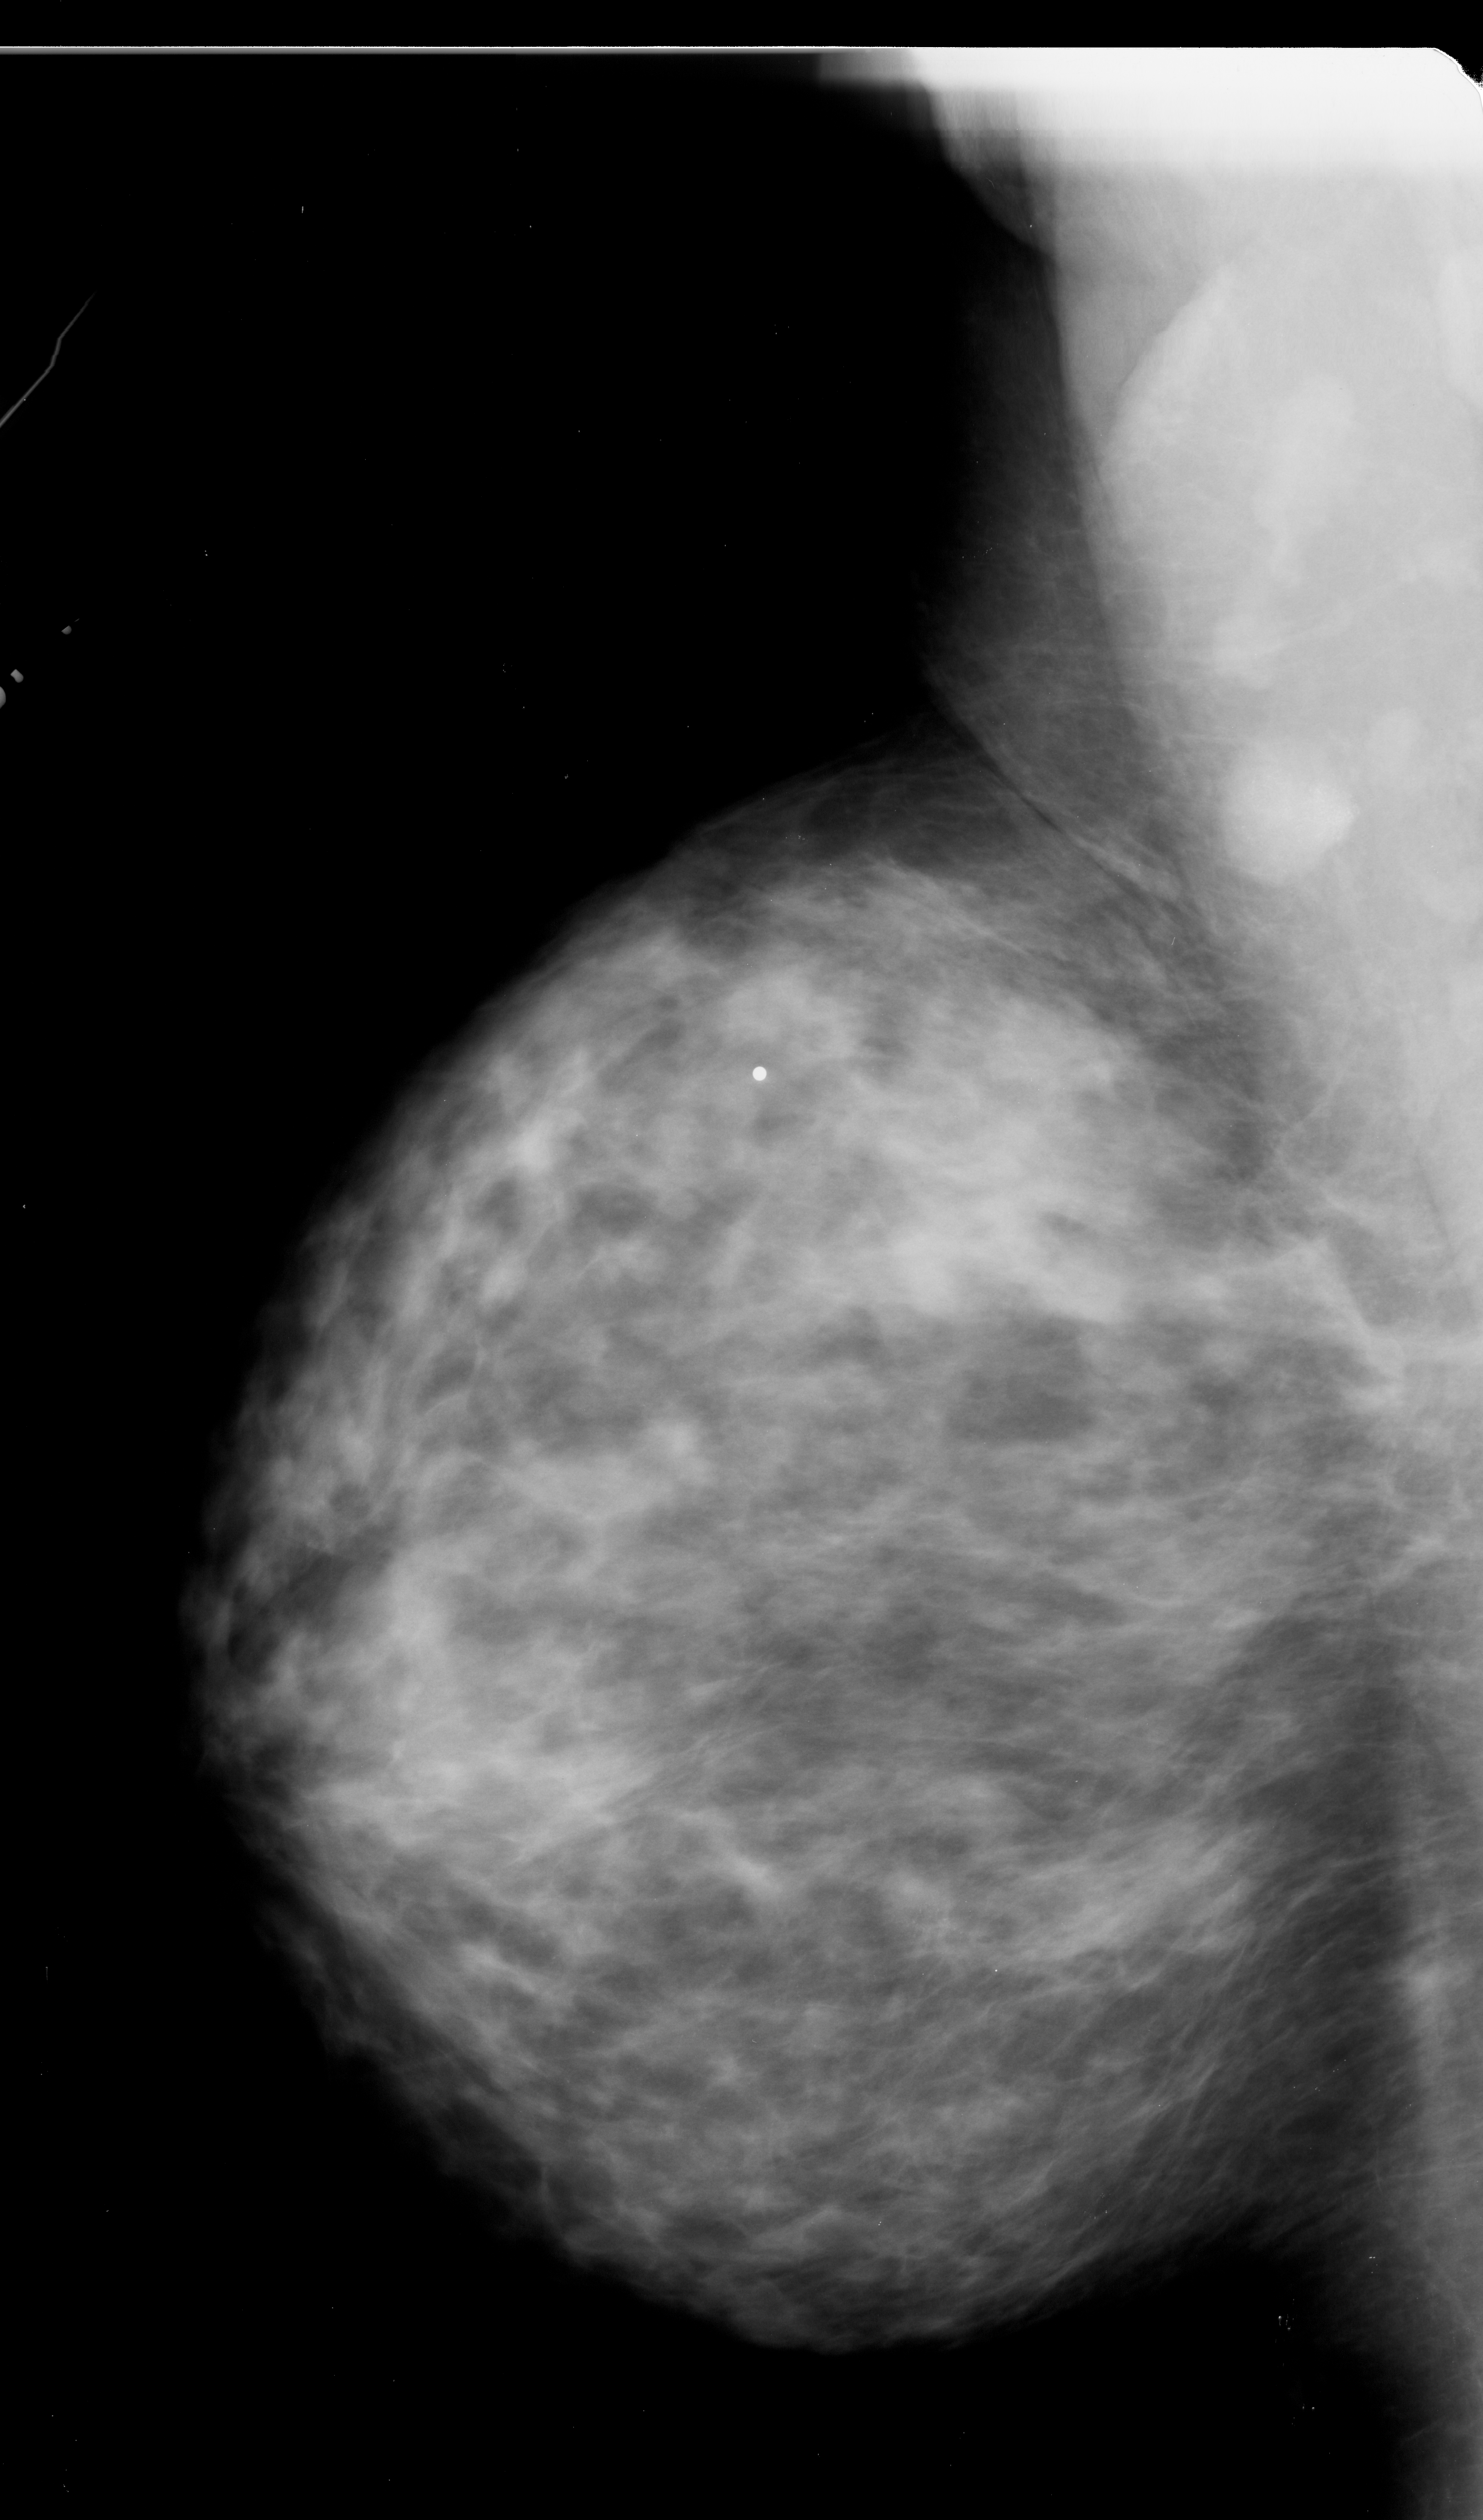
Scanned film-screen mammogram; left breast; mediolateral oblique (MLO) view; breast composition: extremely dense (BI-RADS density category 4 of 4).
Abnormality record for this image: calcifications, morphology pleomorphic, distribution clustered; BI-RADS assessment category 4; pathology result (as recorded, not read from the image): malignant.